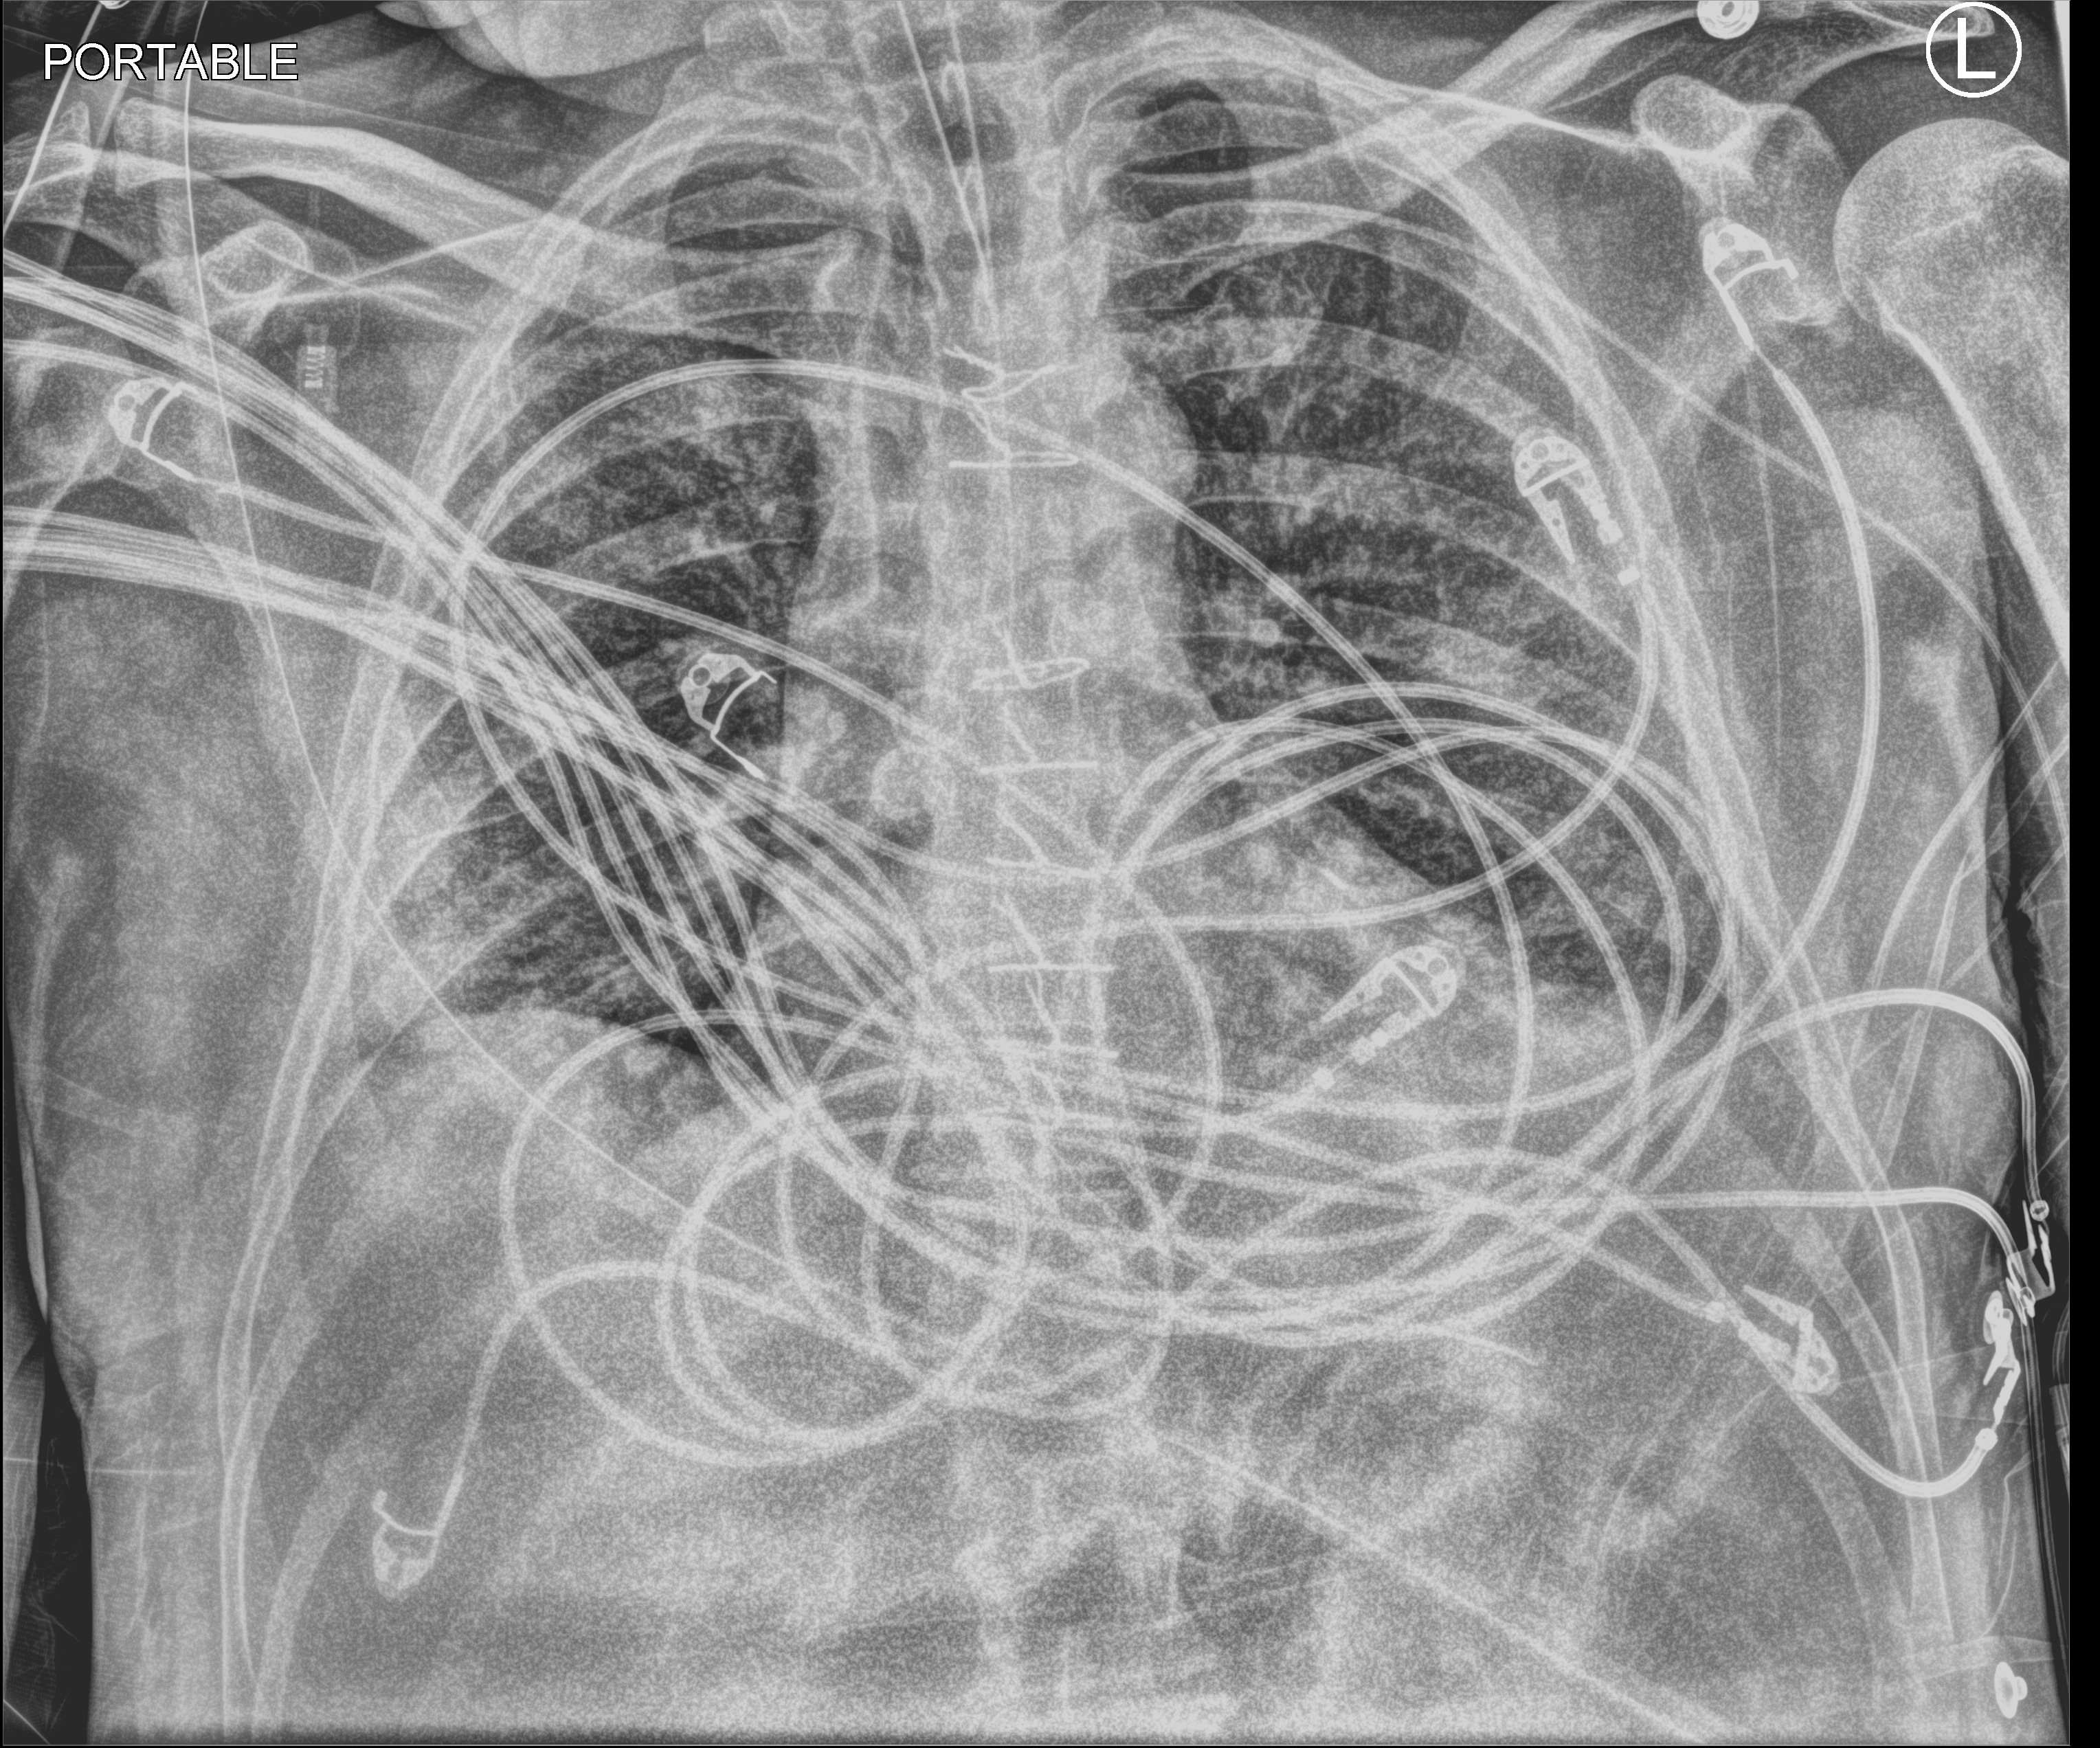
Bedside chest radiograph (computed radiography), anteroposterior (AP) projection. Patient hospitalised with COVID-19; male, aged 18–59 years.
From the hospital-stay record, not from the radiograph (when in the stay this image was taken is not recorded): hypertension (admission record): no; mechanically ventilated during this hospital stay: yes; admitted to intensive care during this hospital stay: yes.